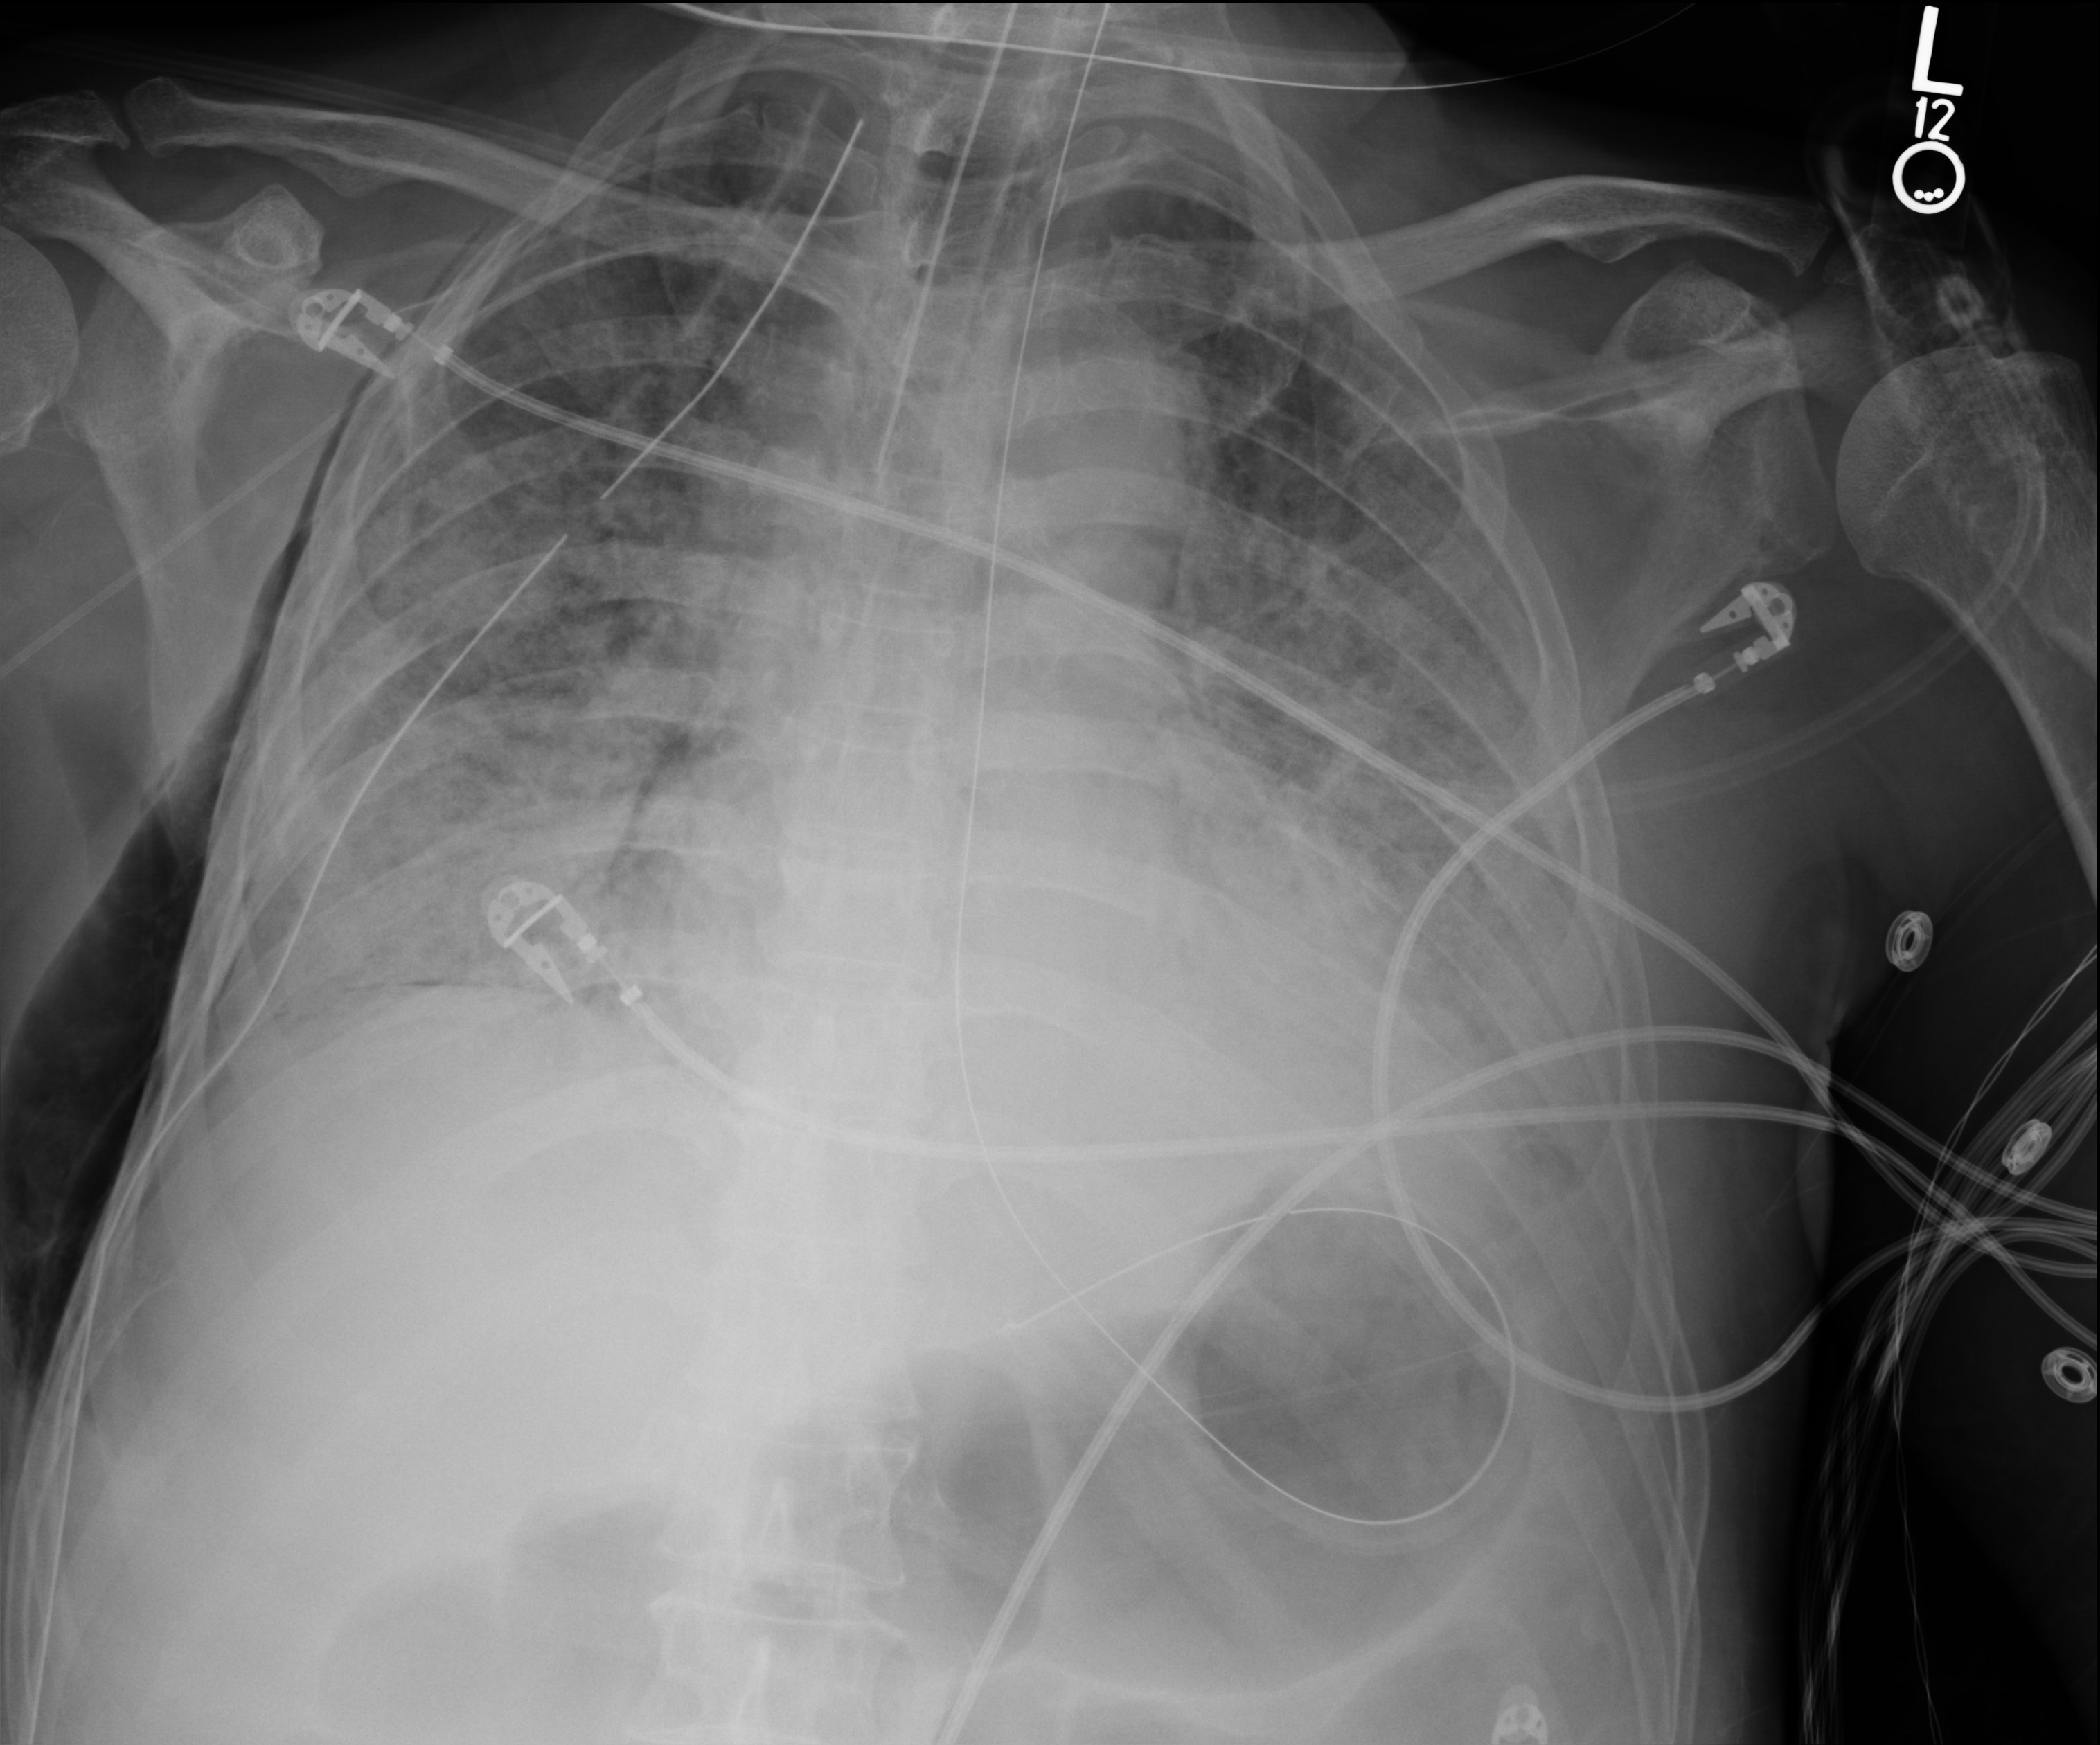
Chest X-ray (portable), anteroposterior (AP) projection. Patient hospitalised with COVID-19; male, aged 60–74 years.
Admission-level facts for this patient (not findings on this image; timing relative to this image not recorded):
- length of hospital stay: 37 days
- mechanically ventilated during this hospital stay: yes
- admitted to intensive care during this hospital stay: yes